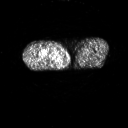
FDG PET of an extremity soft-tissue mass (from a PET/CT study), one axial slice; slice 238 of 311 in the series (ordered by position); 128 × 128 image matrix, field of view 700 × 700 mm. Patient: male, 50 years. From the clinical record (not read from this slice): histological type: undifferentiated - pleiomorphic; grade: high; site of the primary tumour: right thigh.
Annotated regions visible in this slice (expert contour drawn on MRI and transferred to this co-registered scan by the dataset authors):
- gross tumour volume including surrounding oedema: bounding box <41,50,56,60> (left, top, right, bottom; pixels)